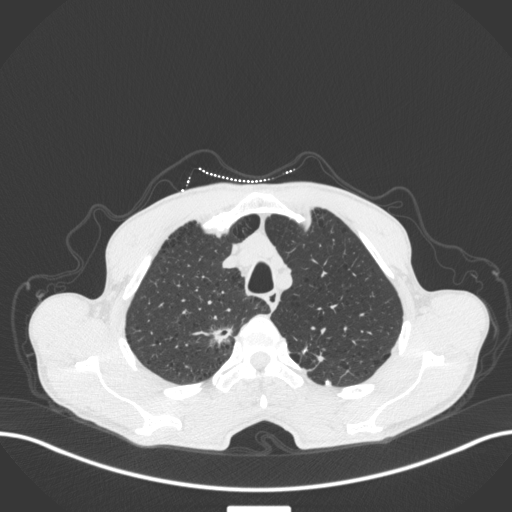
Chest CT, one axial slice. Slice 353 of 445 in the series (ordered by position). Reconstruction kernel B31f. 120 kVp. Lung window (W 1500 / L -600 HU). 1 mm slice thickness. 512 × 512 image matrix, field of view 400 × 400 mm. Male patient, age 70 years. Case-level facts recorded for this patient, not image findings: clinical TNM (as recorded): T1a N0 M0.
Structures marked on this image (rectangle marked by the reading radiologist):
- lung tumour (recorded histology: adenocarcinoma): box from (x=194, y=319) to (x=235, y=353) px